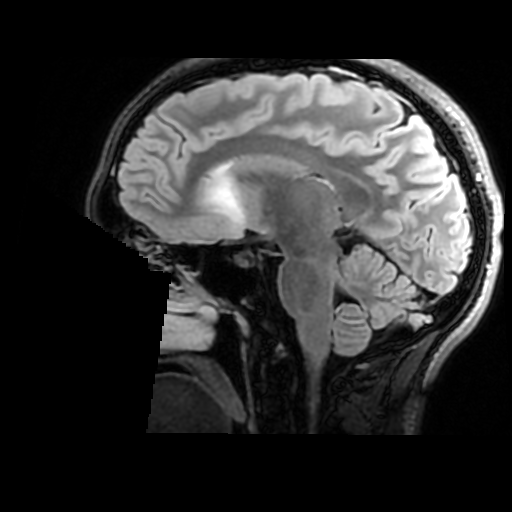
Brain MRI from a brain-tumour surgery series, one sagittal slice; T2 FLAIR; 1 mm slice thickness; 512 × 512 image matrix, field of view 240 × 240 mm. Case-level facts recorded for this patient, not image findings: histopathology: Astrocytoma; WHO grade: 2; IDH mutation: yes; tumour location: Right Insular.
Outlined on this slice (outlined manually by an expert reader):
- tumour: bounding box (x1, y1, x2, y2) in pixels: (200, 174, 243, 222)